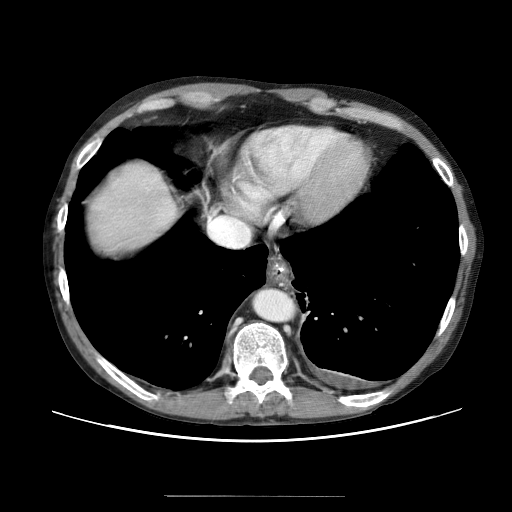
Contrast-enhanced abdominal CT (liver protocol), one axial slice. Position 58 of 69 along the scan axis. Reconstruction kernel STANDARD. 120 kVp. Soft-tissue window (W 400 / L 40 HU). 512 × 512 image matrix. Case-level facts recorded for this patient, not image findings: diagnosis: hepatocellular carcinoma (patient treated with transarterial chemoembolisation; whether this scan precedes or follows treatment is not stated here); TNM stage (as recorded): Stage-IVB; Child-Pugh class: B.
Annotated regions visible in this slice (semi-automatic segmentation, software-assisted and operator-edited):
- liver parenchyma outside the tumour (the mass and vessels are separate outlines, so this box may not span the whole liver): box from (x=80, y=158) to (x=184, y=272) px
- liver vessels: (x=120, y=188)–(x=141, y=198)